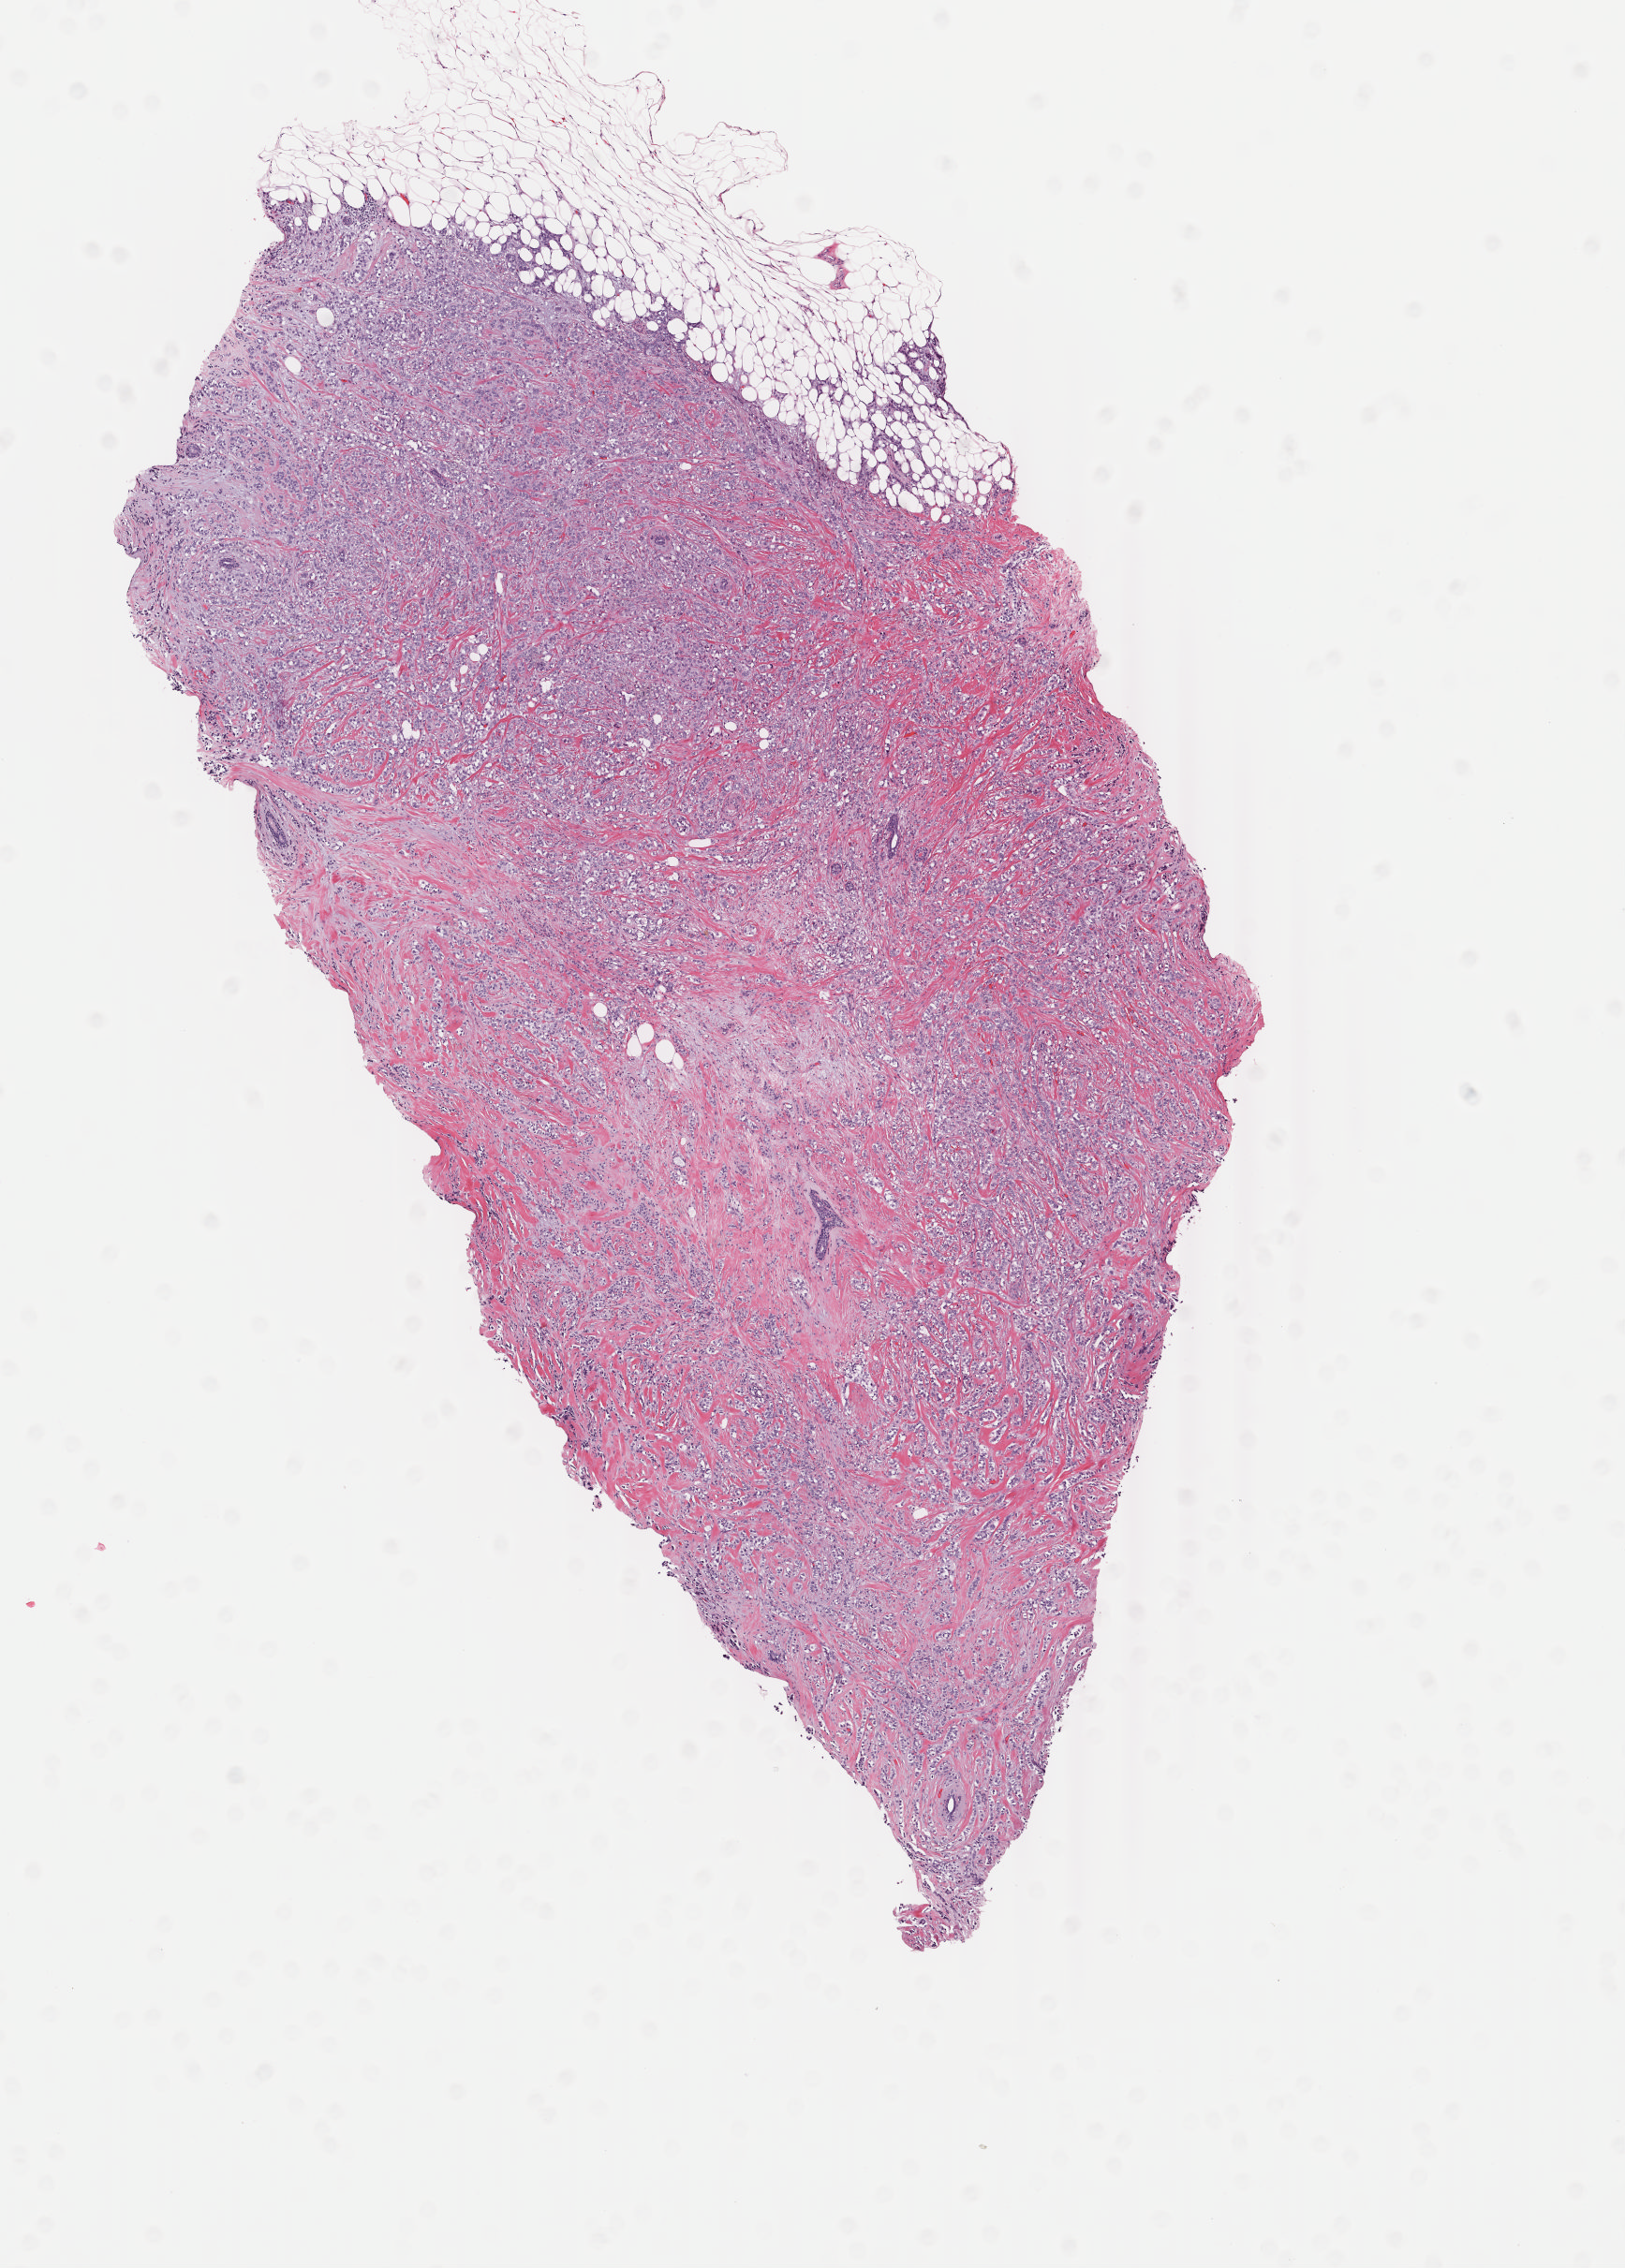
Digitized H&E tissue section (whole slide) — whole scanned area (about 6.9 x 9.6 mm, slide scanned at 40x) shown as a low-resolution overview. Frozen section. Breast, primary tumour sample. Female, age 71 years at initial diagnosis. Slide review estimates, as recorded: tumour cells 80%, tumour nuclei 80%, normal cells 0%, stromal cells 20%, necrosis 0%. Inflammatory infiltration, as recorded: lymphocyte infiltration 40%, monocyte infiltration 20%, neutrophil infiltration 20%.
- laterality: left
- diagnosis: Lobular carcinoma, NOS
- TNM: T3 N1a MX
- AJCC pathologic stage: IIIA